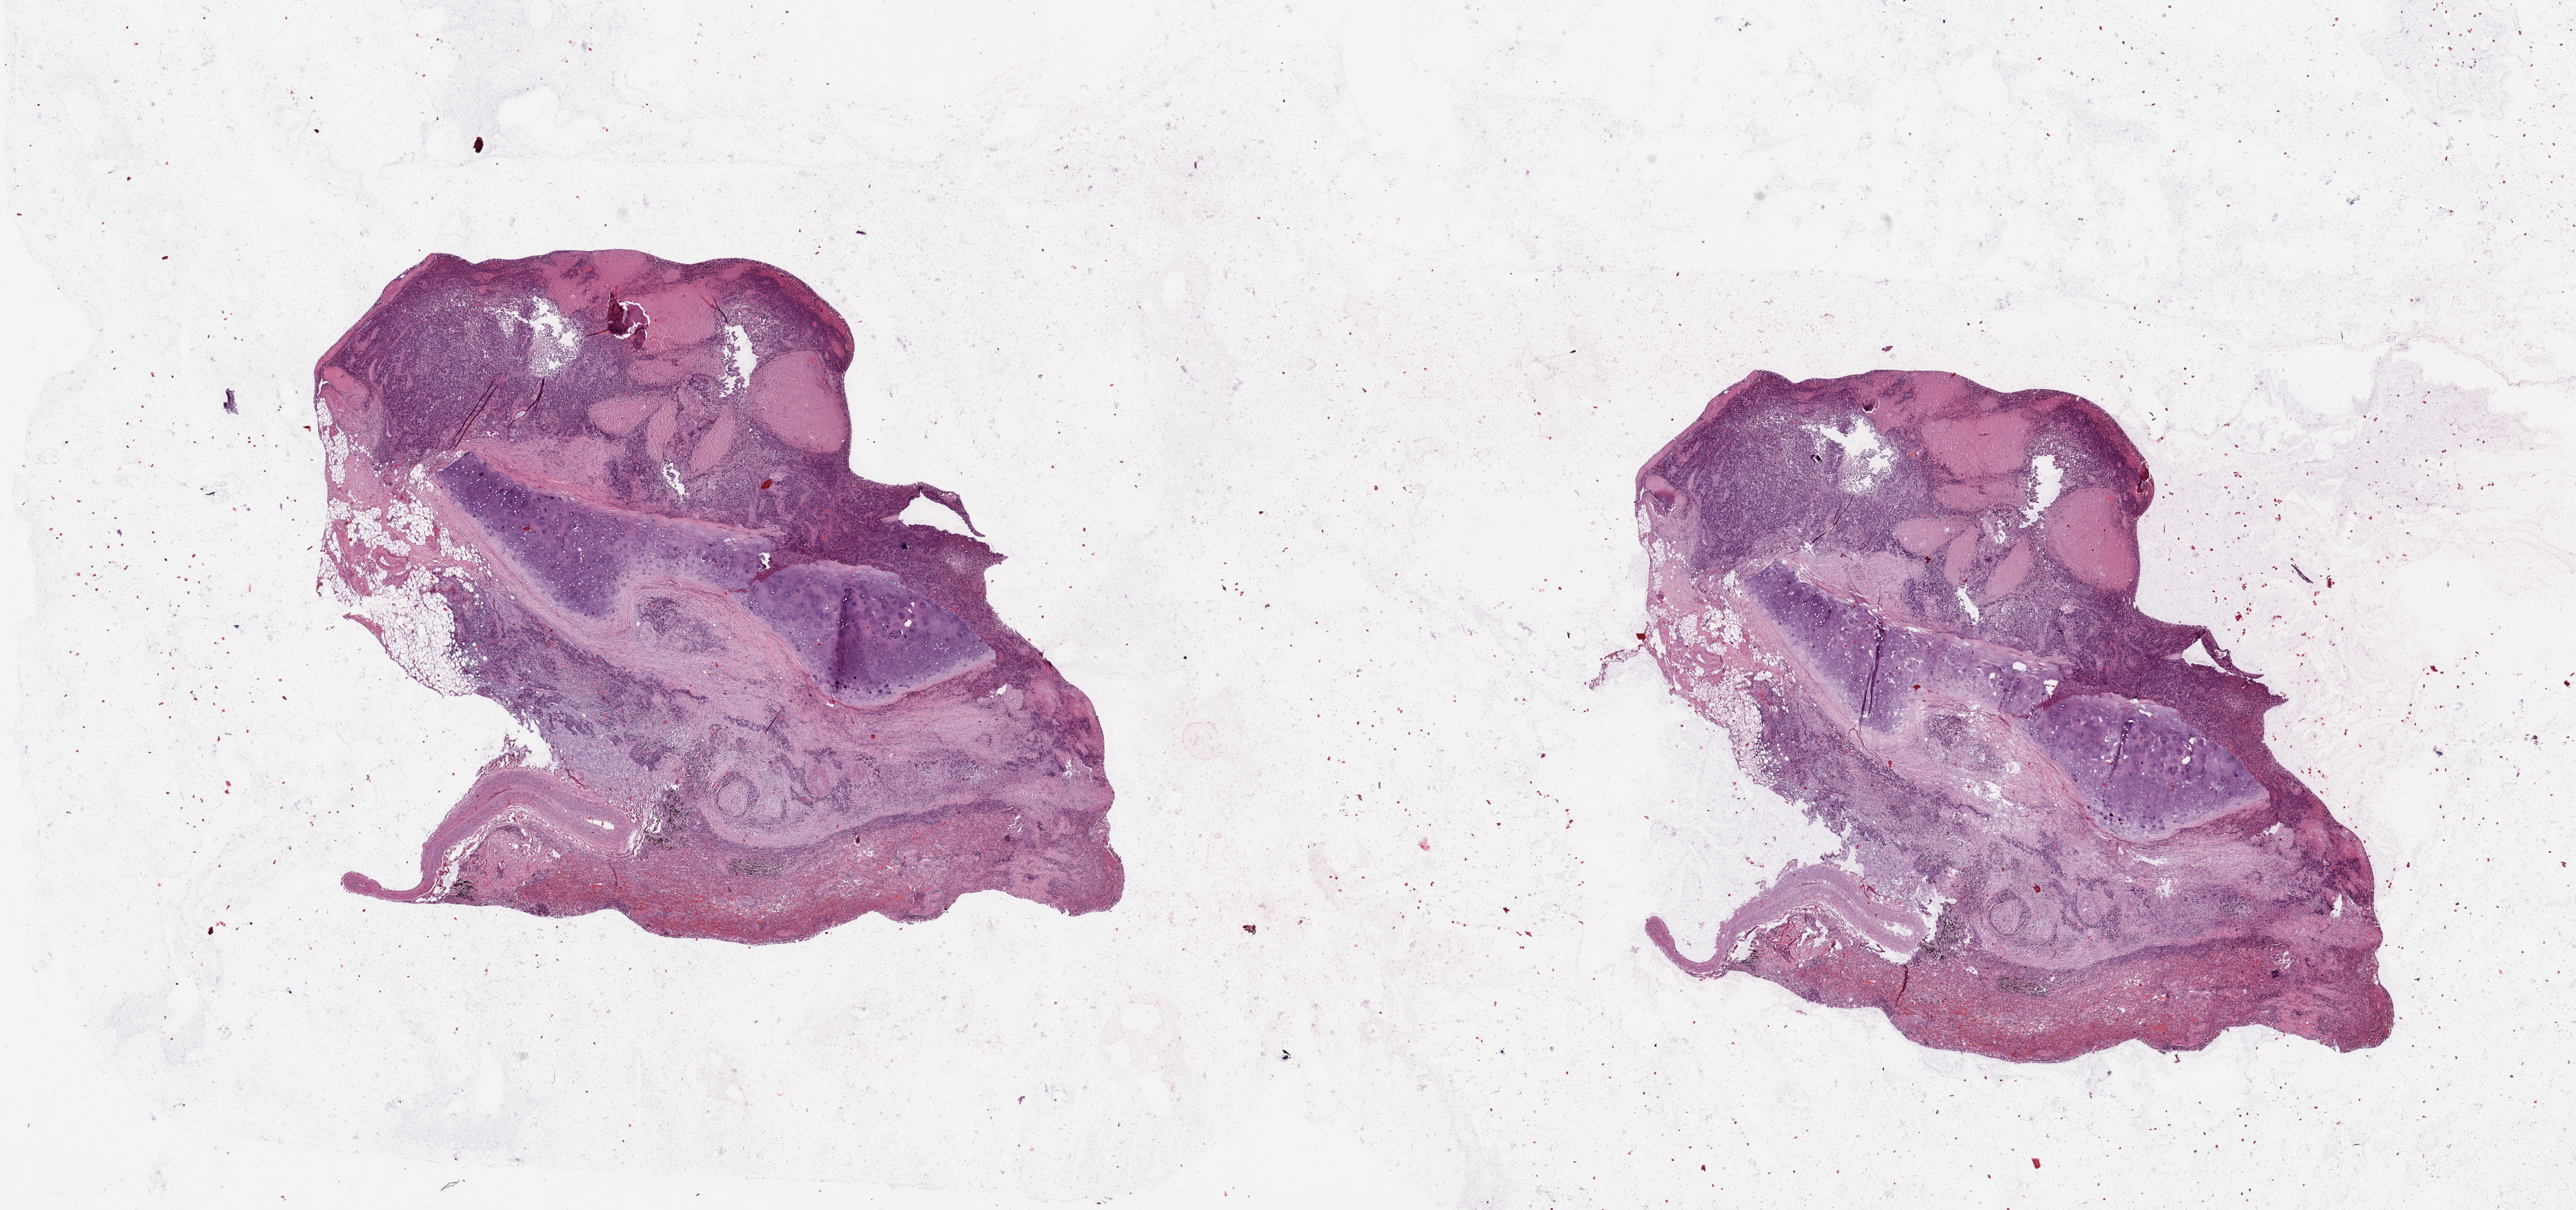
Whole-slide histology image, Hematoxylin and eosin (H&E) stained — a low-resolution overview of the entire scanned area, about 29.5 x 13.9 mm, tumour tissue sample, lung. 72-year-old male patient. Histologic grade: G3 (poorly differentiated).
AJCC pathologic stage: IIIA. Histologic diagnosis: Squamous cell carcinoma, NOS.